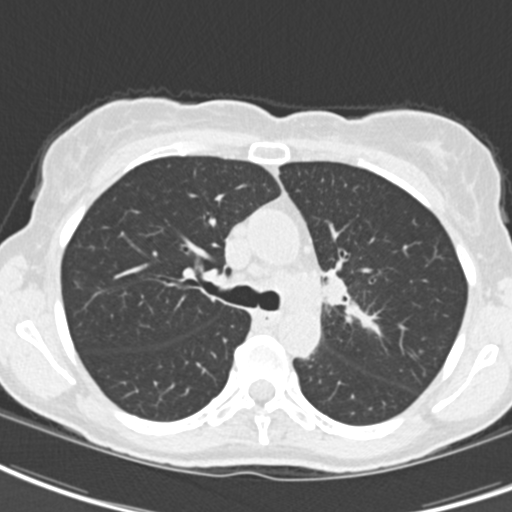
Low-dose screening chest CT, one axial slice; slice 133 of 189 in the series (ordered by position); reconstruction kernel B30f; 120 kVp; lung window (W 1500 / L -600 HU); 2 mm slice thickness; 512 × 512 image matrix.
Structures marked on this image (outlined manually by an expert reader):
- lesion 2 (tumor, hilum of left lung): bounding box (x1, y1, x2, y2) in pixels: (322, 275, 346, 306)